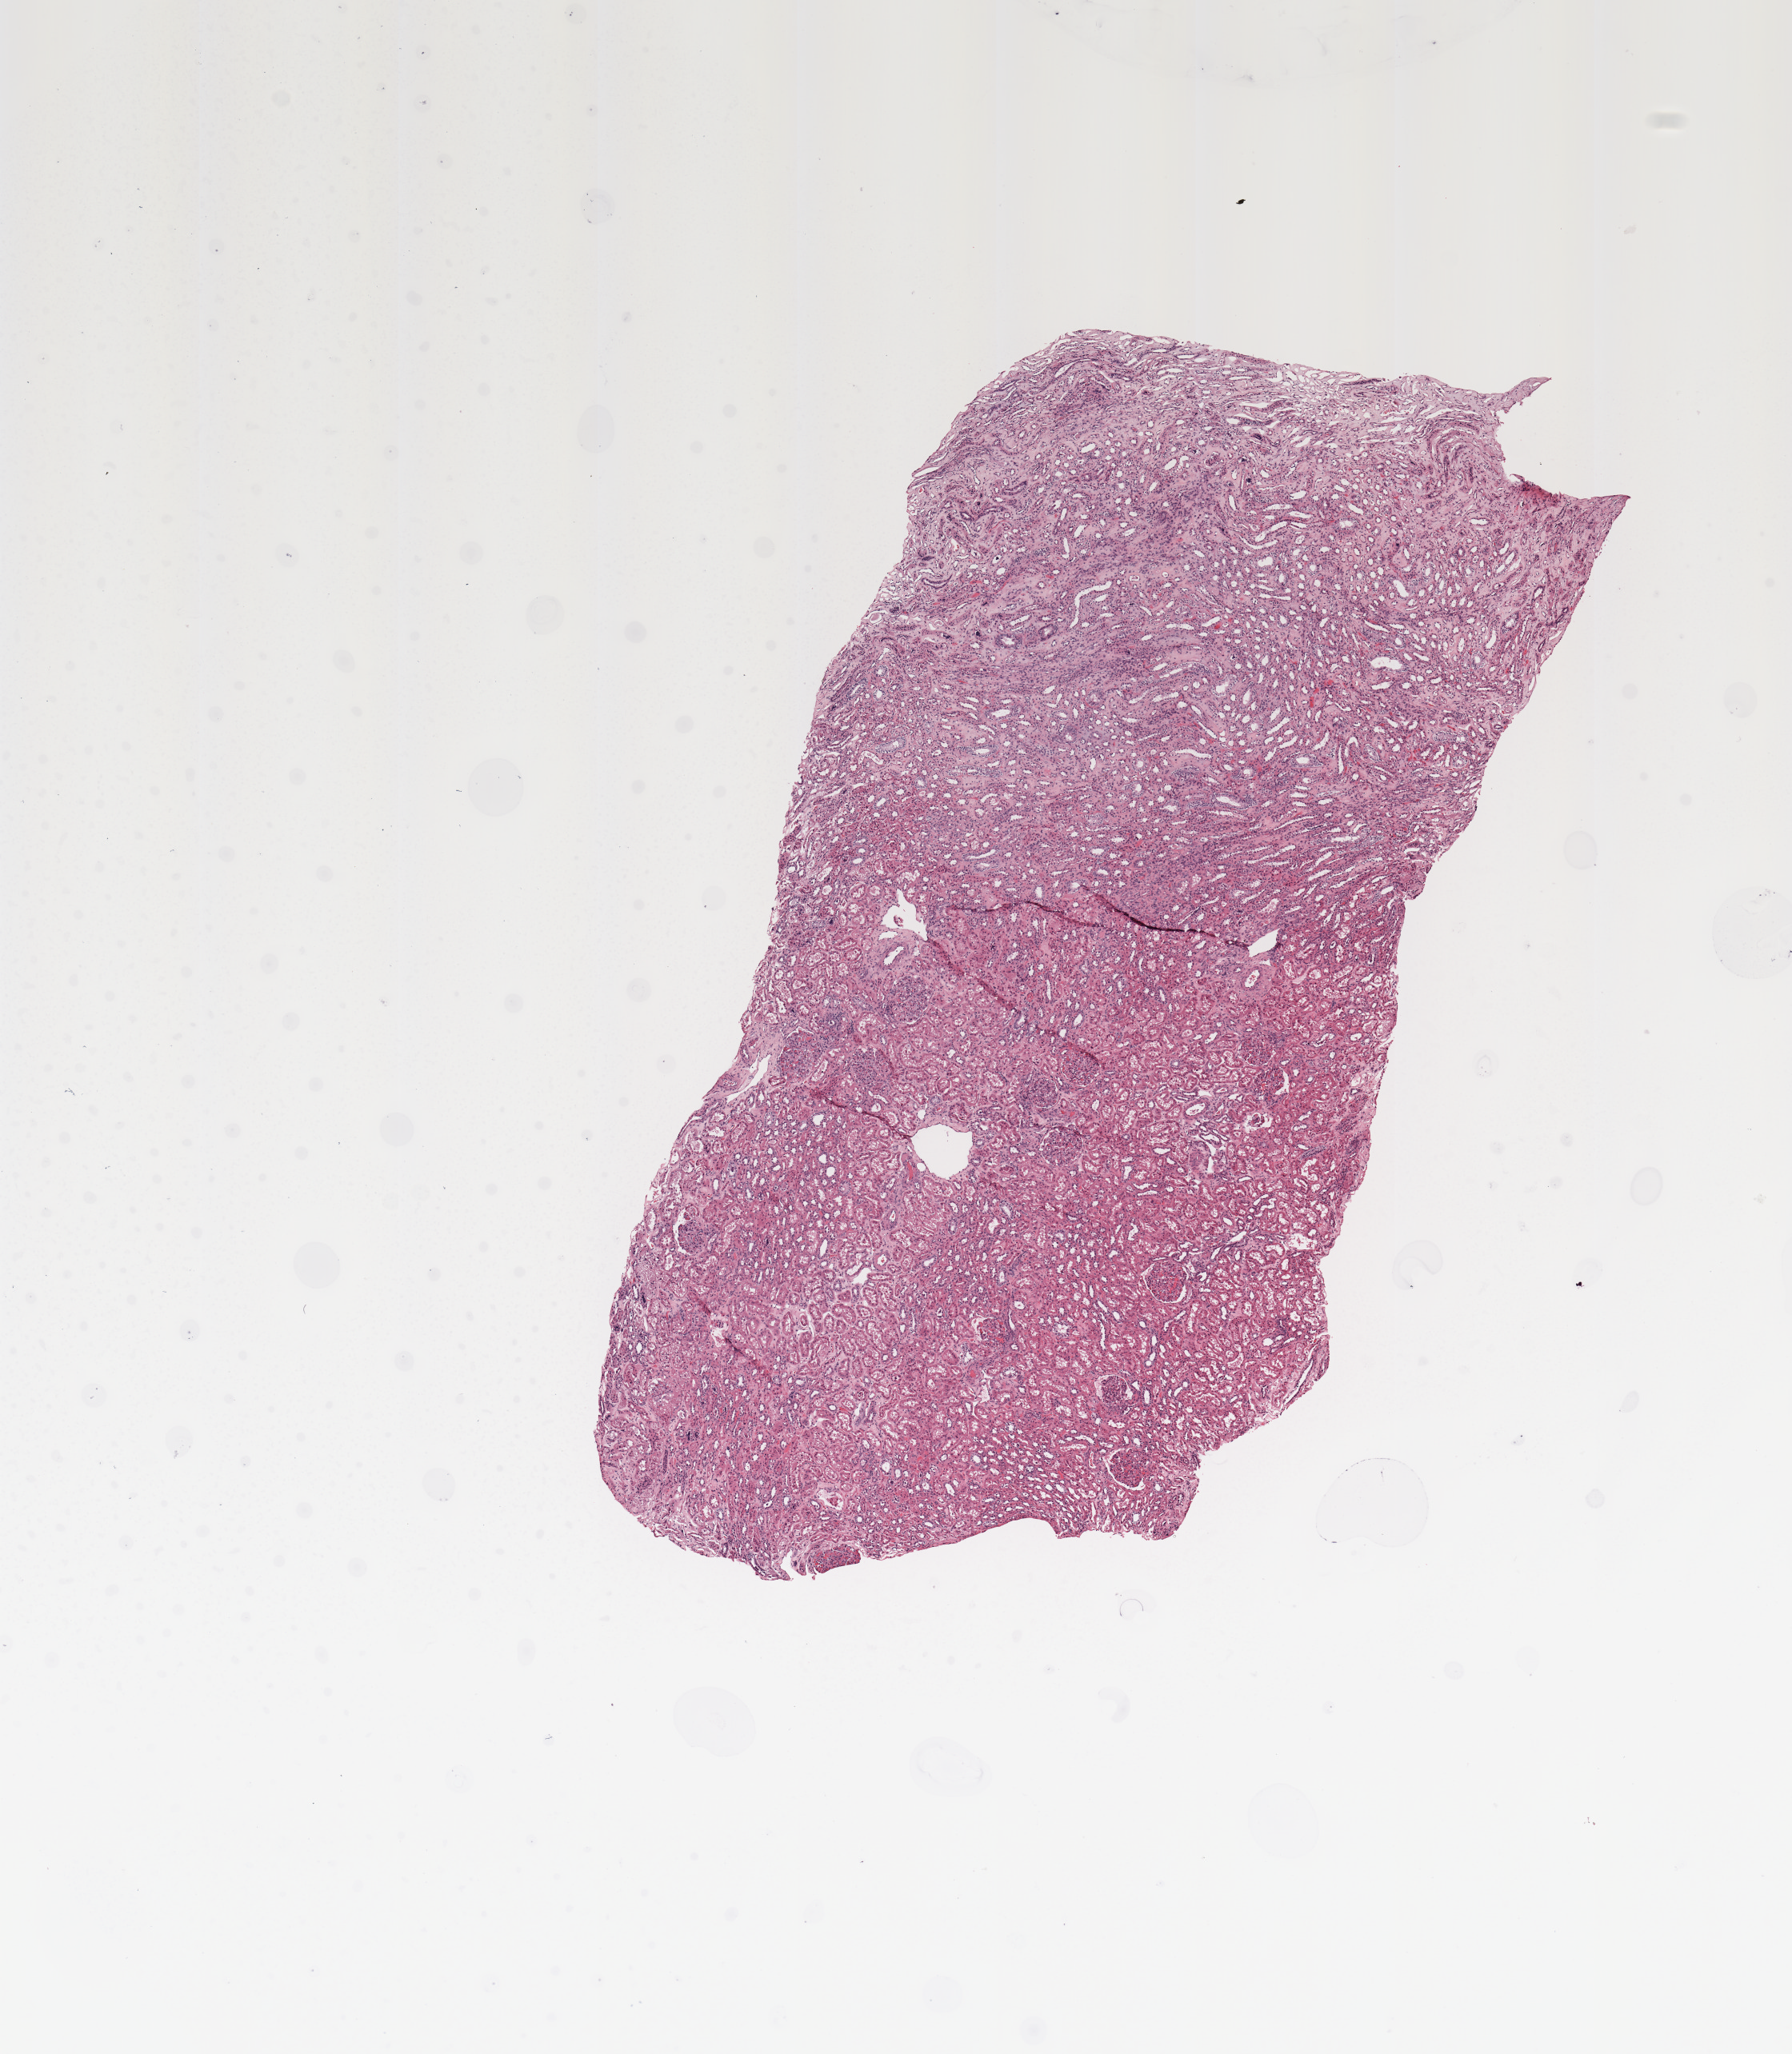
Digitized H&E tissue section (whole slide) — low-resolution overview of the scanned area, about 8.9 x 10.2 mm (acquisition: 20x scan). Normal (non-tumour) tissue sample, sampled site: kidney. Male, 53 y/o.
* this section: normal (non-tumour) tissue from the same patient
* patient diagnosis: Renal cell carcinoma, NOS